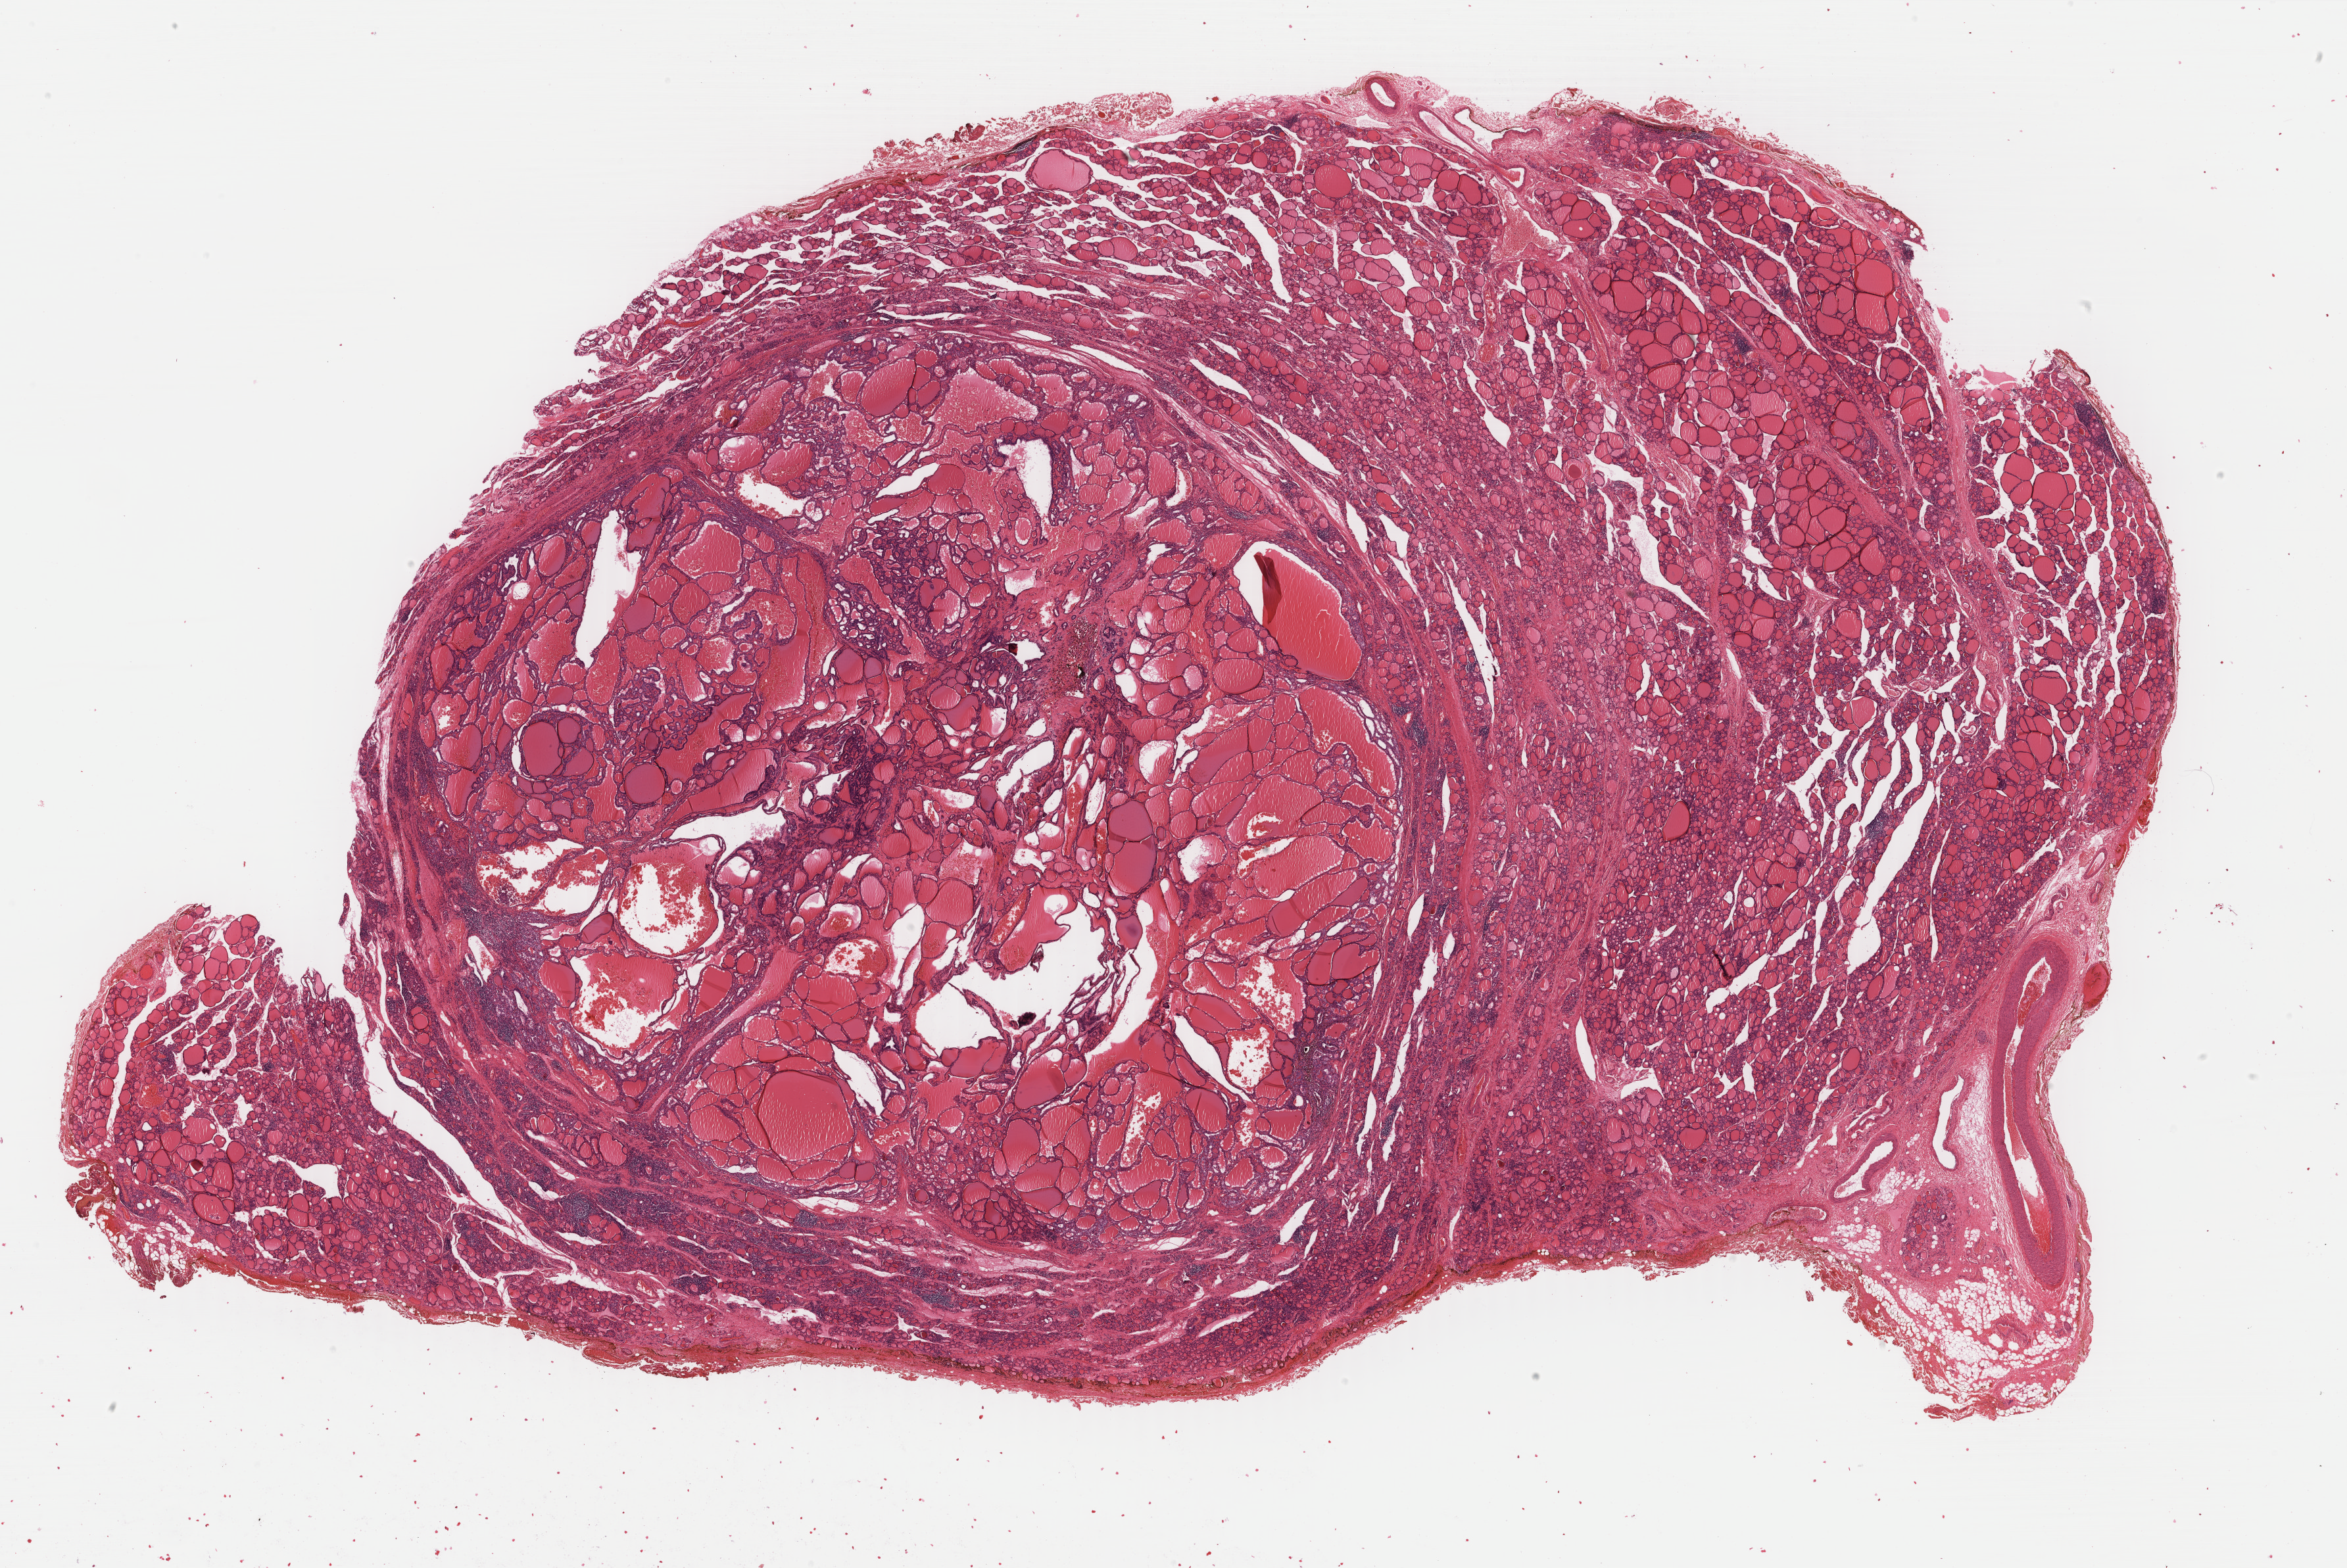
H&E whole-slide image — low-resolution overview of the scanned area, about 28.3 x 18.9 mm. Formalin-fixed paraffin-embedded (FFPE) diagnostic section. Sample: primary tumour, thyroid. Female patient; age at initial diagnosis 39 years.
AJCC pathologic stage: I (7th edition). Laterality: right. Histologic diagnosis: Papillary carcinoma, follicular variant (thyroid gland). Lymph nodes positive (case pathology): 0 of 1 examined.